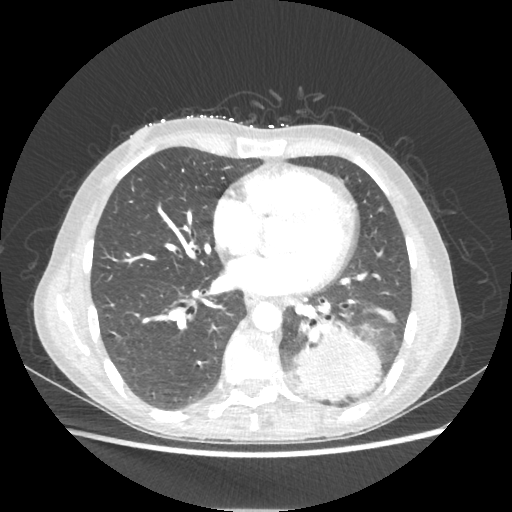
Chest CT, one axial slice. Position 94 of 221 along the scan axis. 80 kVp. Lung window (W 1500 / L -600 HU). 1.25 mm slice thickness. 512 × 512 image matrix, field of view 360 × 360 mm. Patient: female, 53 years. Case-level facts recorded for this patient, not image findings: clinical TNM (as recorded): T3 N0 M0.
Structures marked on this image (bounding box drawn by a radiologist):
- lung tumour (recorded histology: adenocarcinoma): bounding box <293,319,381,402> (left, top, right, bottom; pixels)